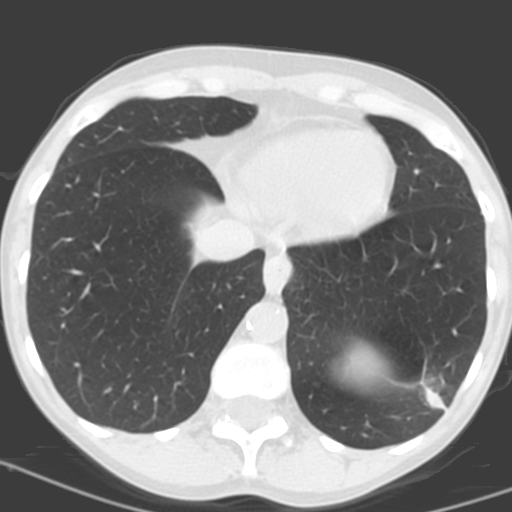
Low-dose screening chest CT, one axial slice. Slice 42 of 156 in the series (ordered by position). 120 kVp. Lung window (W 1500 / L -600 HU). 512 × 512 image matrix, field of view 262 × 262 mm.
Annotated regions visible in this slice (outlined manually by an expert reader):
- lesion 1 (tumor, lower lobe of left lung): bounding box (x1, y1, x2, y2) in pixels: (424, 389, 447, 411)